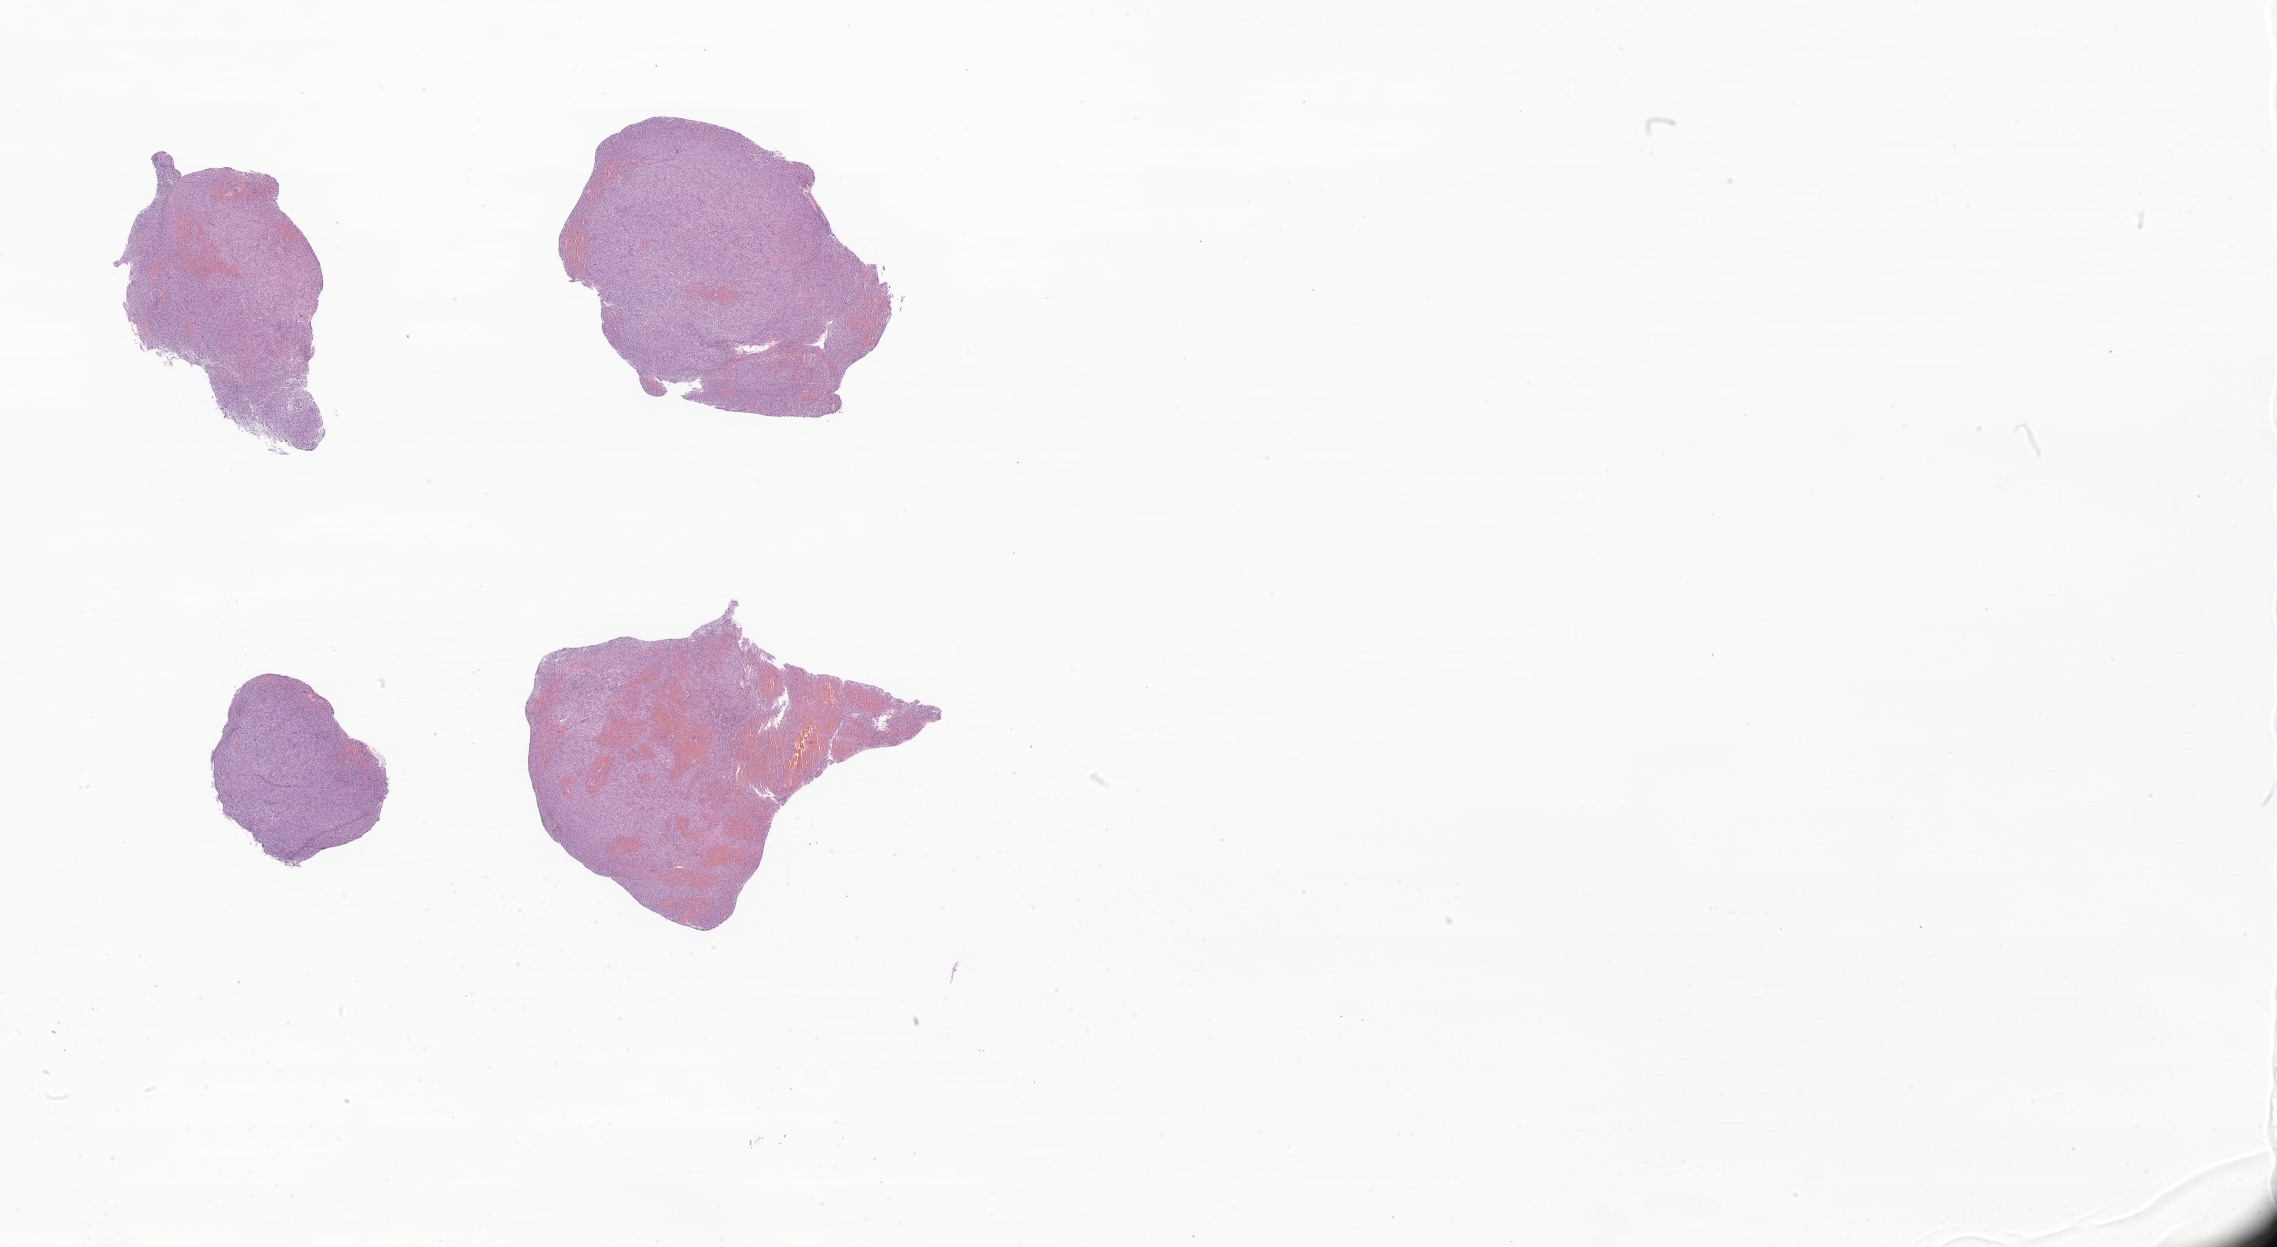
Digitized haematoxylin and eosin-stained section of tumor tissue from the brain — shown as a low-resolution overview of the whole scanned area (about 38.4 x 21.0 mm), formalin-fixed paraffin-embedded section. Patient: male, age 575 days (about 1.6 years).
Diagnosis: Neoplasm, malignant.